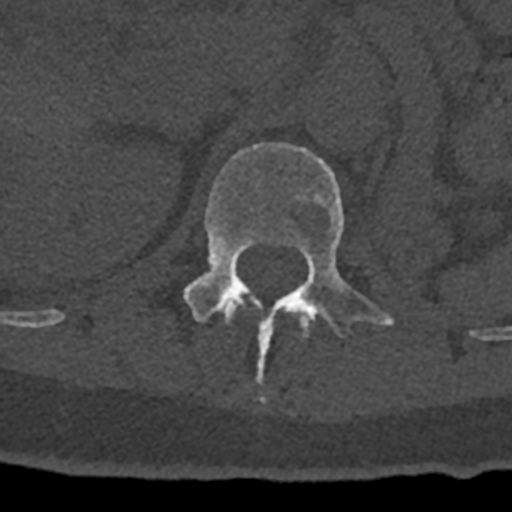
CT including the spine, one axial slice. Position 446 of 797 along the scan axis. Reconstruction kernel Br40s/3. 120 kVp. Bone window (W 1800 / L 400 HU). 0.5 mm slice thickness. 512 × 512 image matrix. Male patient, age 74 years. Case-level facts recorded for this patient, not image findings: primary cancer: renal; vertebrae with lytic lesions (as recorded): T10, L1, L2, L3, L4, L5.
Annotated regions visible in this slice (semi-automatically segmented with operator editing):
- L1 vertebra: bounding box <183,143,394,403> (left, top, right, bottom; pixels)
- T12 vertebra: <220,297,314,337>